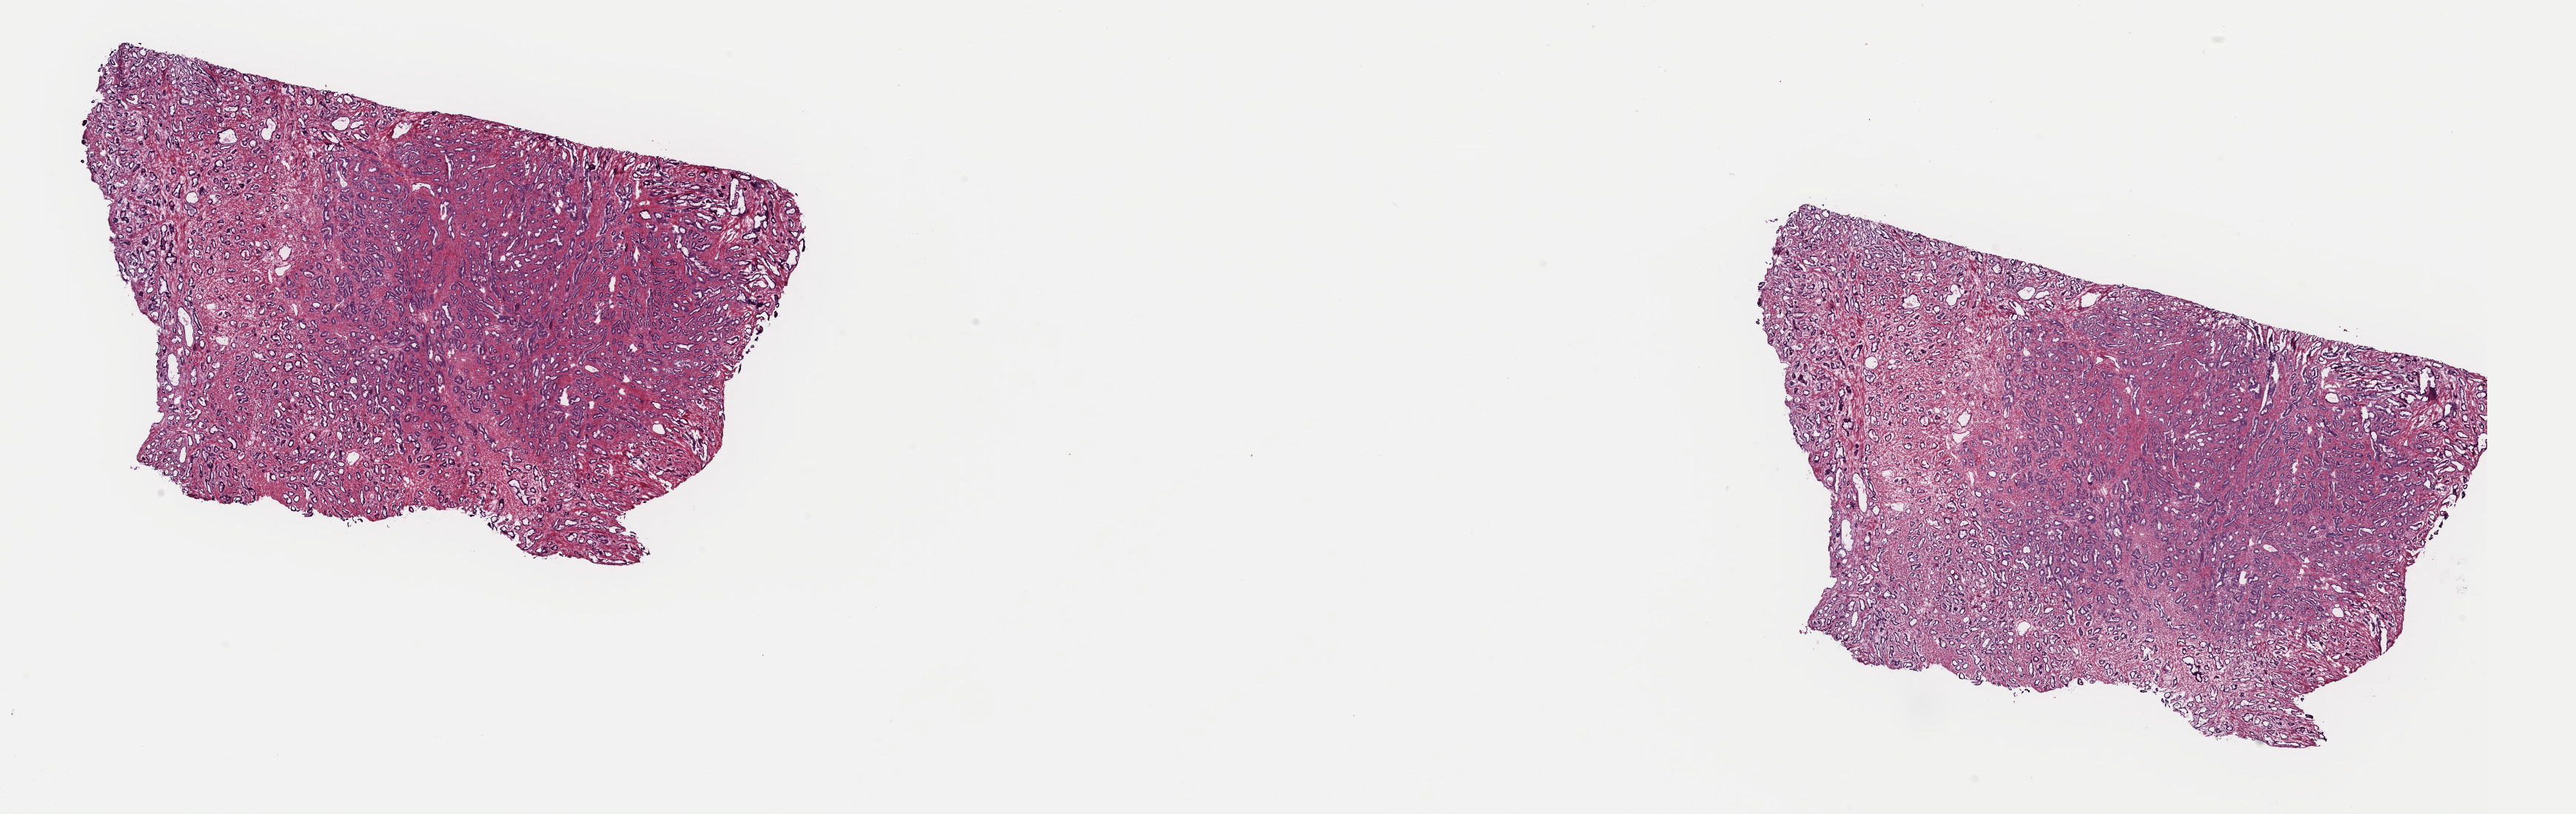
Whole-slide histology image, H&E — shown as a low-resolution overview of the whole scanned area (about 27.5 x 8.7 mm, acquisition: 40x scan); frozen section from the top of the tissue portion; prostate, primary tumour sample. Male patient; age at initial diagnosis 53 years. Gleason score: 7 (3+4). Pathologist review of this section (percent, as recorded): tumour cells 60%, tumour nuclei 70%, normal cells 5%, stromal cells 35%, necrosis 0%. Infiltration values recorded for this section: lymphocyte infiltration 0%, monocyte infiltration 0%, neutrophil infiltration 0%.
Laterality: bilateral. Pathologic diagnosis: Adenocarcinoma, NOS (prostate gland).